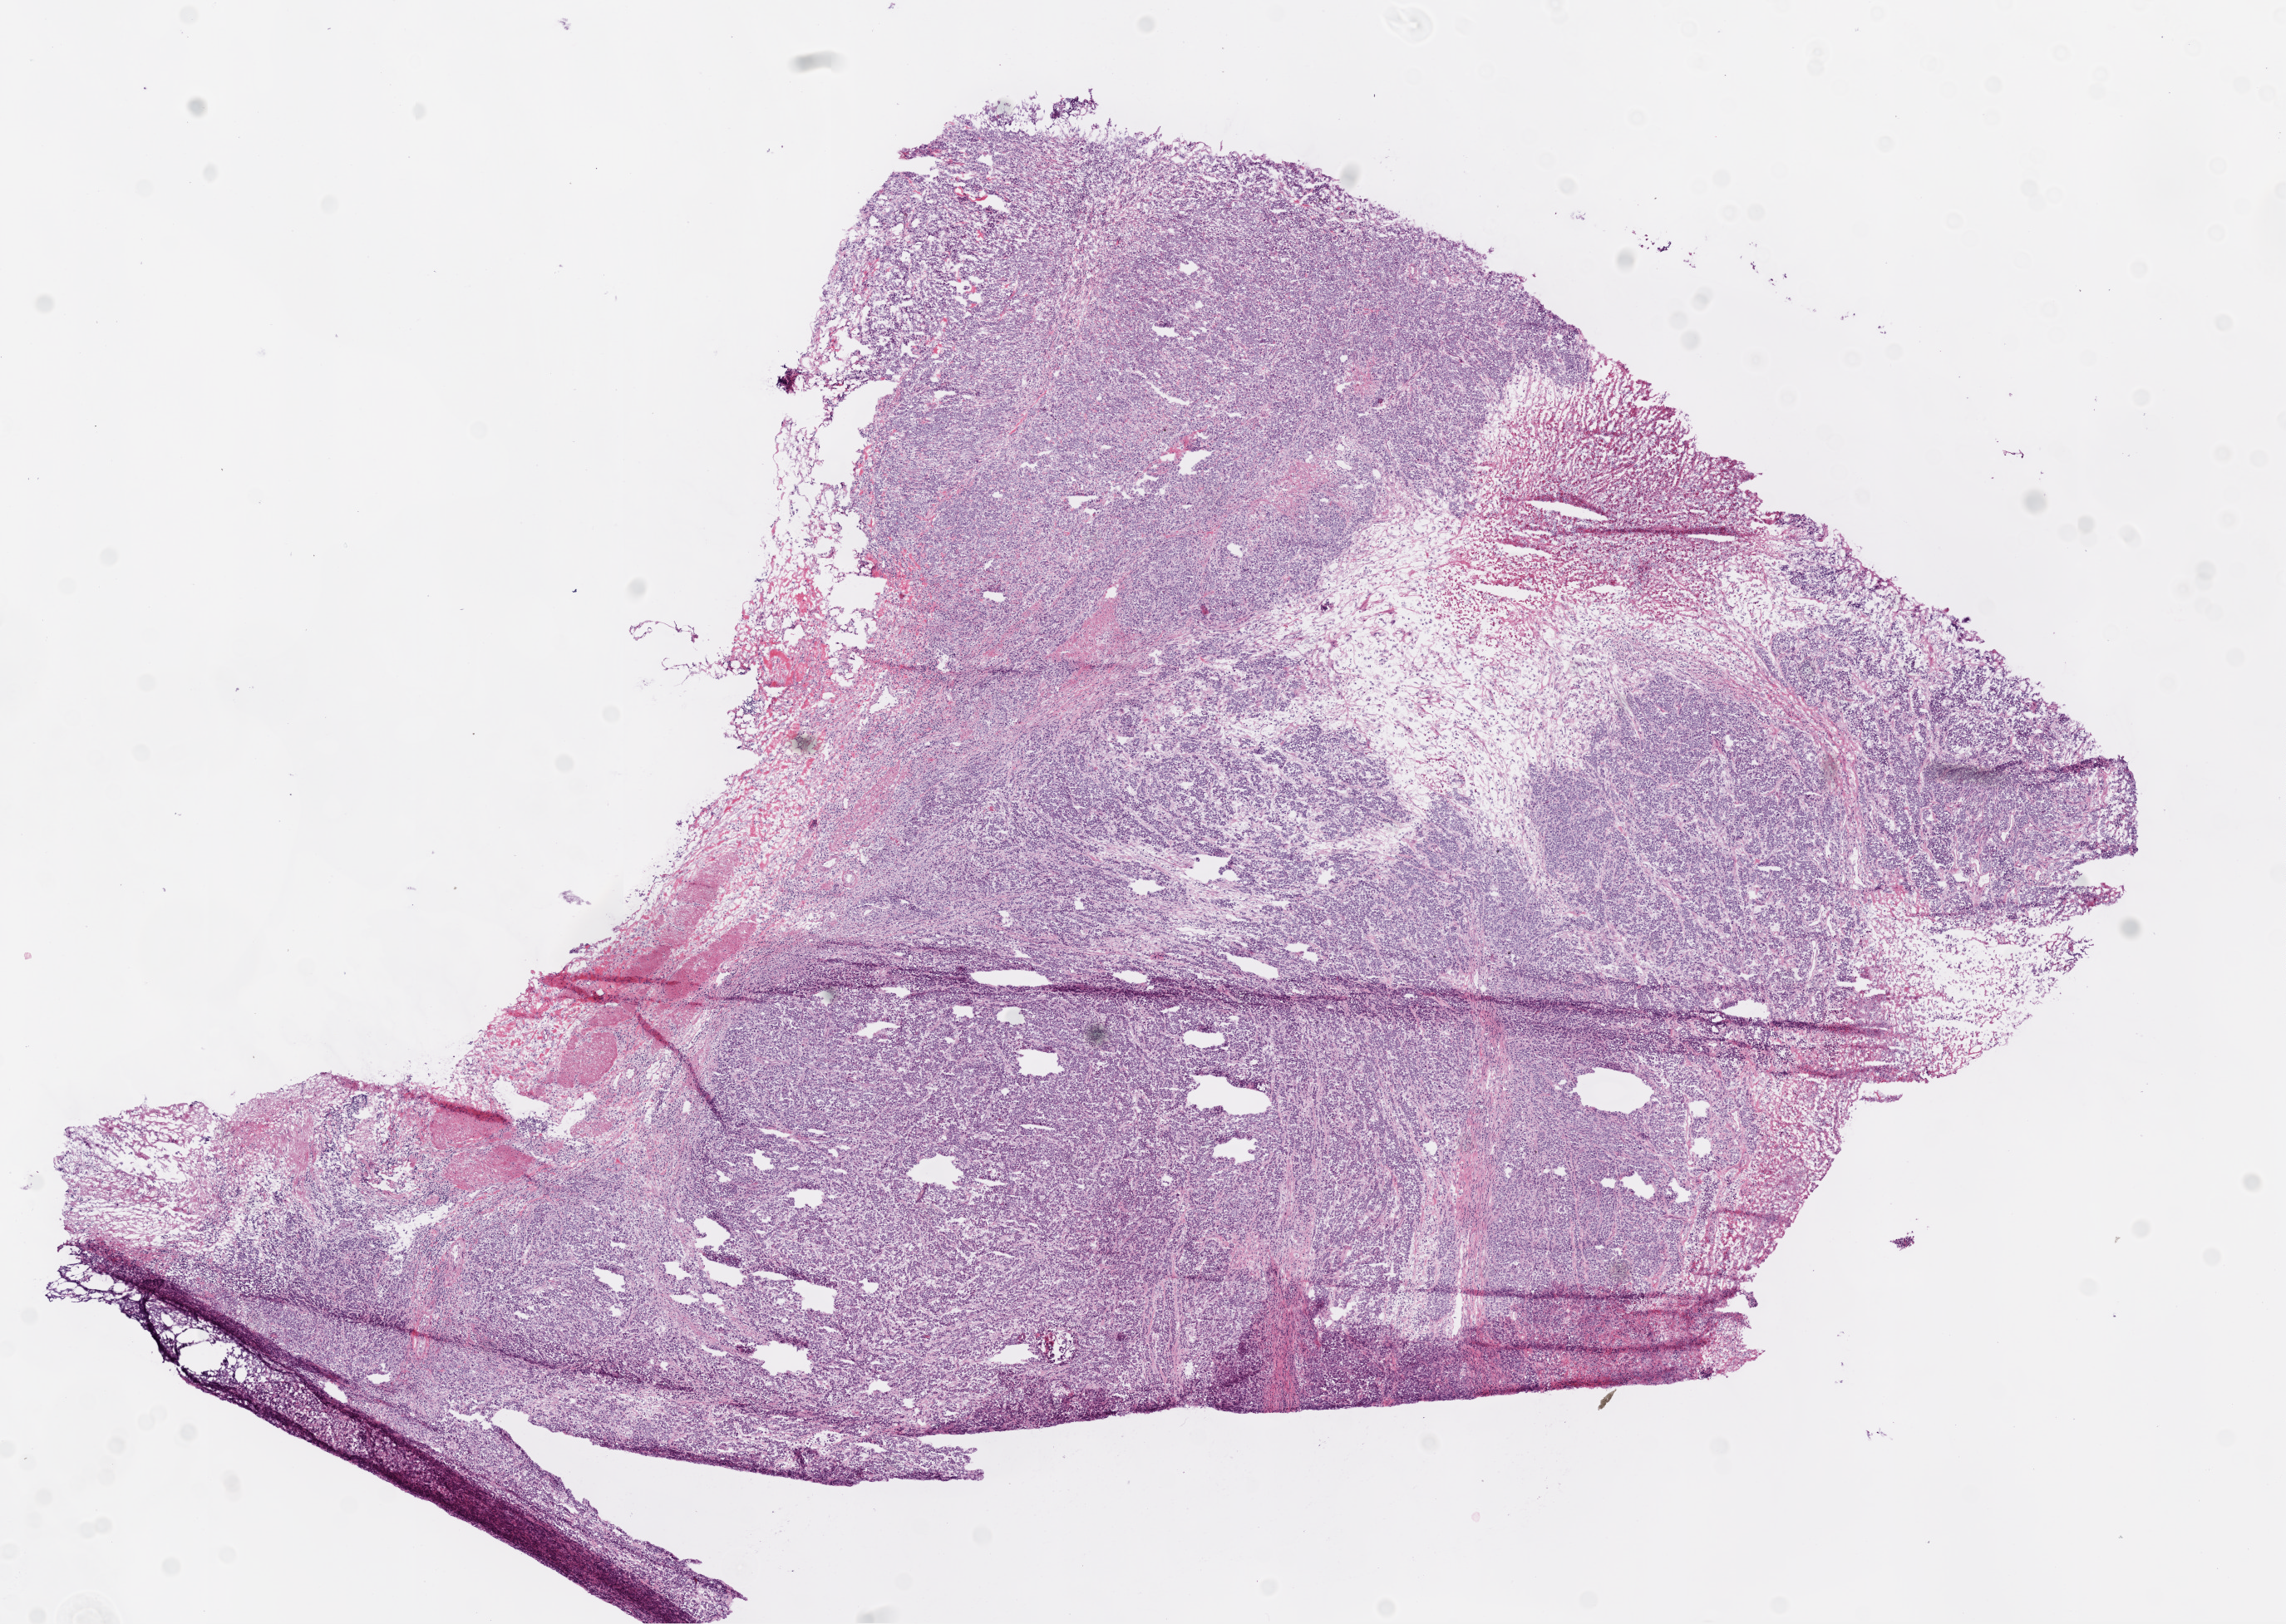
Hematoxylin and eosin (H&E) stained whole-slide image — whole scanned area (about 11.0 x 7.8 mm) shown as a low-resolution overview; frozen section from the bottom of the tissue portion; primary tumour sample from the colon. Female patient; age at initial diagnosis 75 years. Slide review estimates, as recorded: tumour cells 90%, tumour nuclei 90%, normal cells 0%, stromal cells 5%, necrosis 5%.
* pathologic diagnosis: Adenocarcinoma, NOS
* AJCC pathologic stage: IIB (6th edition)